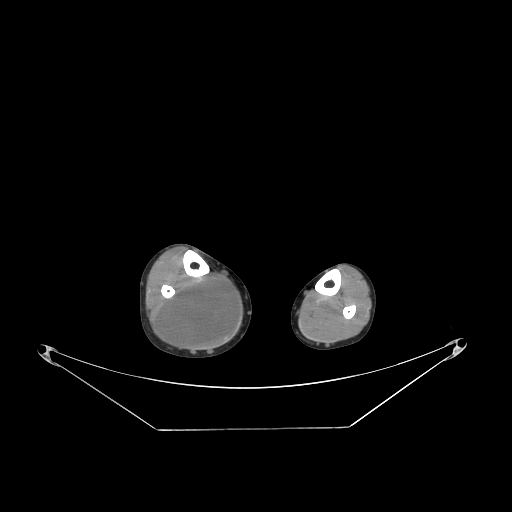
CT of an extremity soft-tissue mass (from a PET/CT study), one axial slice. Slice 86 of 267 in the series (ordered by position). Soft-tissue window (W 400 / L 40 HU). 3.75 mm slice thickness. 512 × 512 image matrix, field of view 500 × 500 mm. Male patient. Case-level facts recorded for this patient, not image findings: histological type: liposarcoma - round cell; grade: high; site of the primary tumour: right calf.
Structures marked on this image (expert contour drawn on MRI and transferred to this co-registered scan by the dataset authors):
- gross tumour volume (mass): box from (x=160, y=276) to (x=239, y=346) px